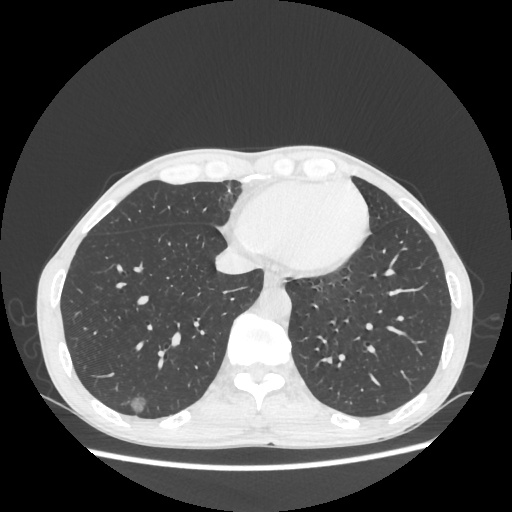
Chest CT, one axial slice; position 79 of 270 along the scan axis; reconstruction kernel STANDARD; lung window (W 1500 / L -600 HU); 1.25 mm slice thickness; 512 × 512 image matrix, field of view 360 × 360 mm. Male patient, age 60 years. Case-level facts recorded for this patient, not image findings: clinical TNM (as recorded): T1c N0 M0.
Annotated regions visible in this slice (bounding box drawn by a radiologist):
- lung tumour (recorded histology: adenocarcinoma): box from (x=120, y=389) to (x=150, y=420) px